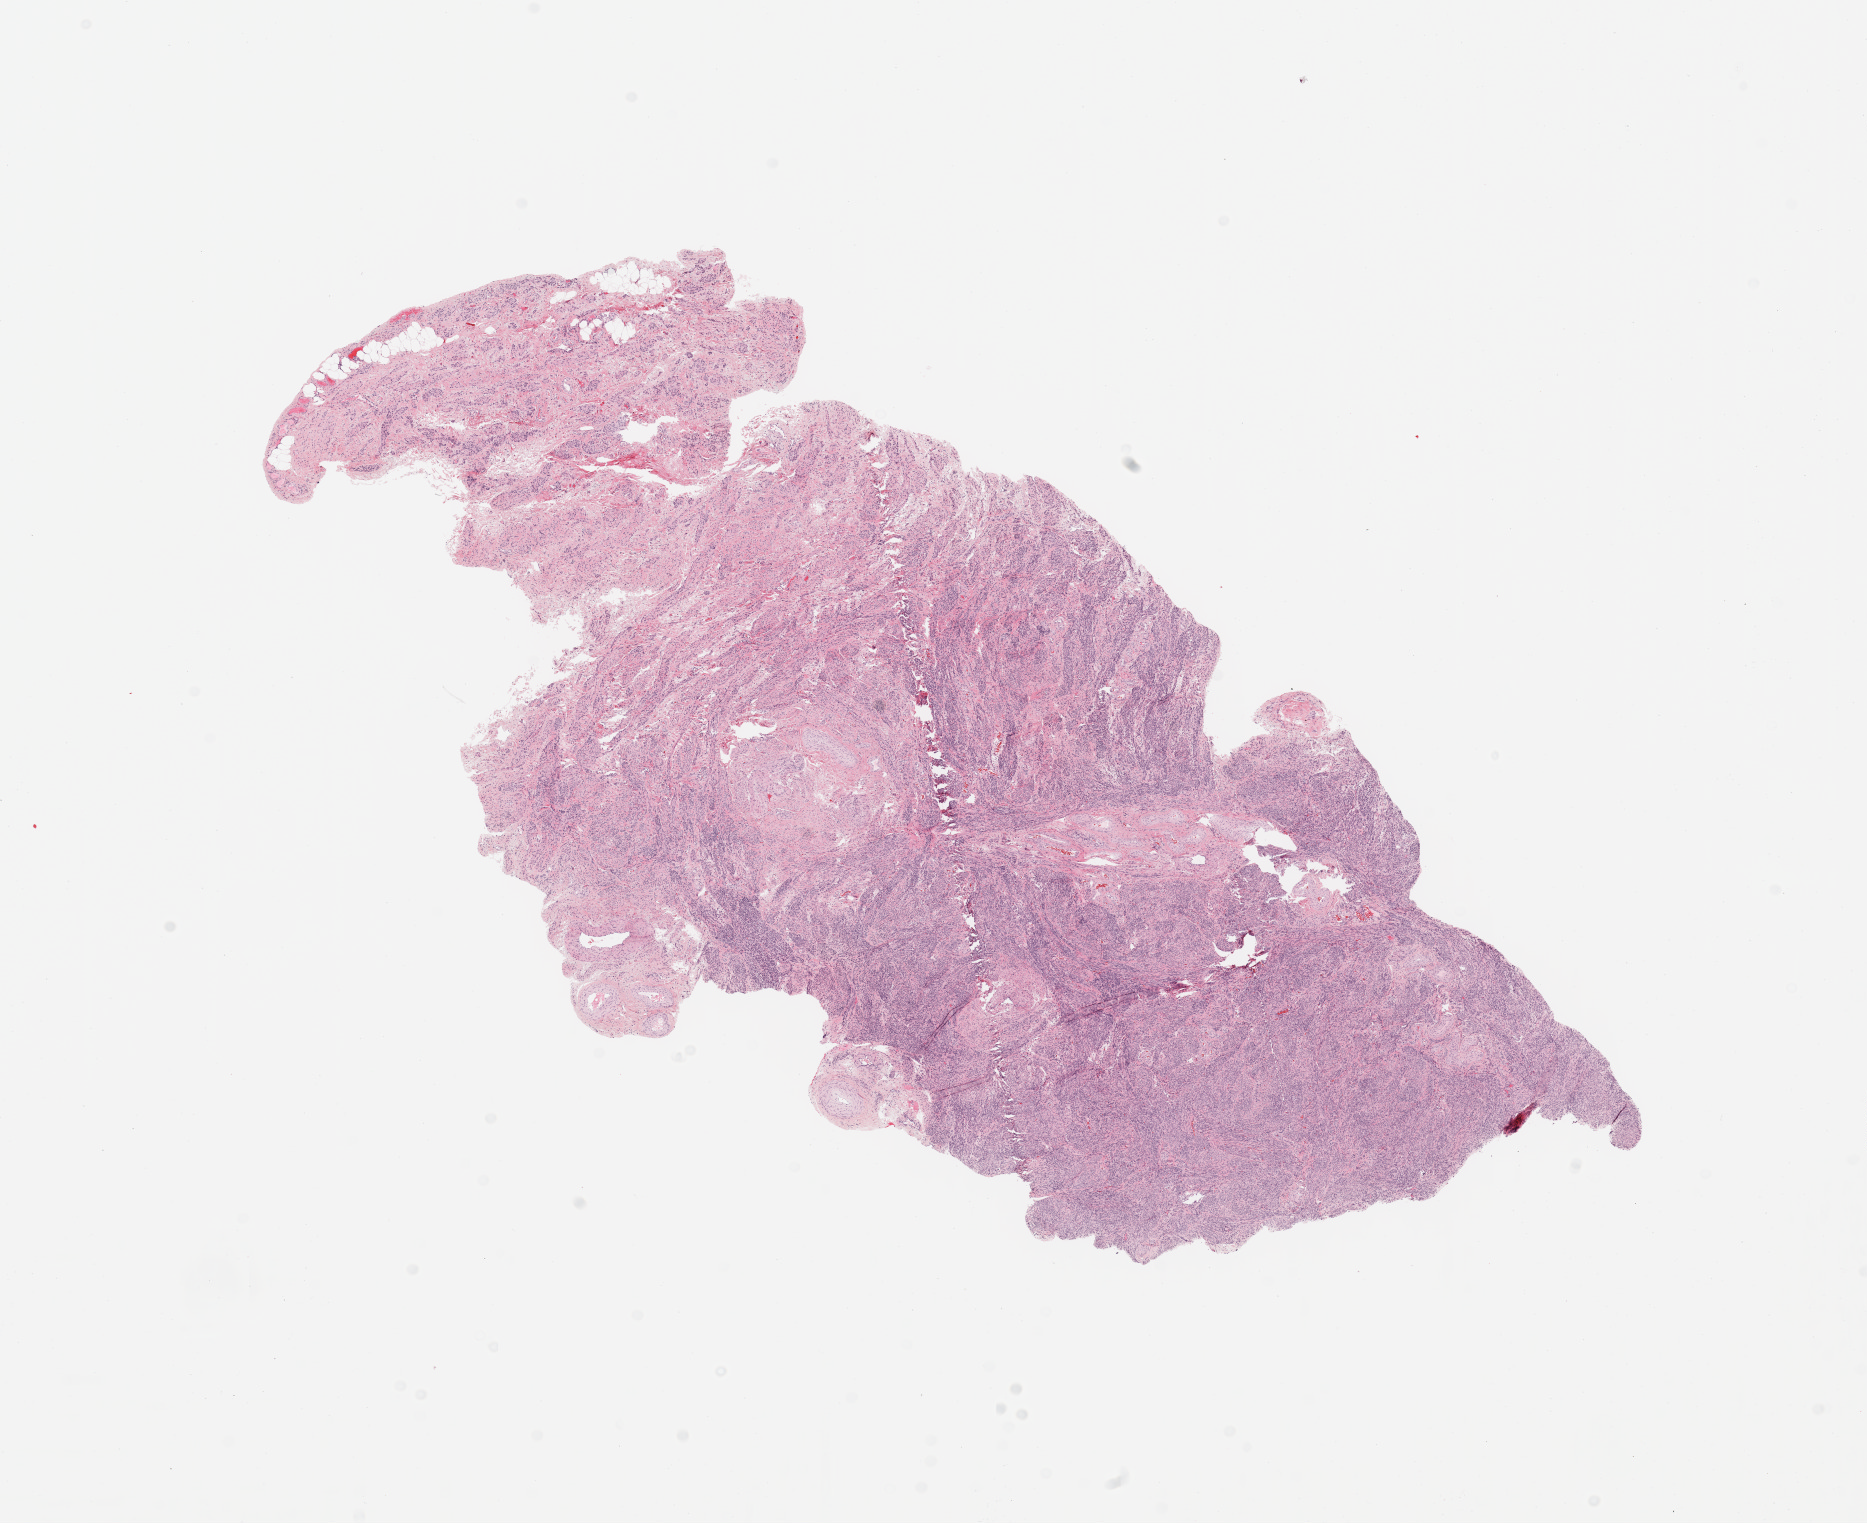
Whole-slide histology image, H&E, shown as a low-resolution overview of the whole scanned area (about 14.8 x 12.0 mm, from a 20x scan); uterus, normal (non-tumour) tissue. Female, 56 y/o.
This section: normal (non-tumour) tissue from the same patient. Patient diagnosis: Endometrioid adenocarcinoma, NOS.